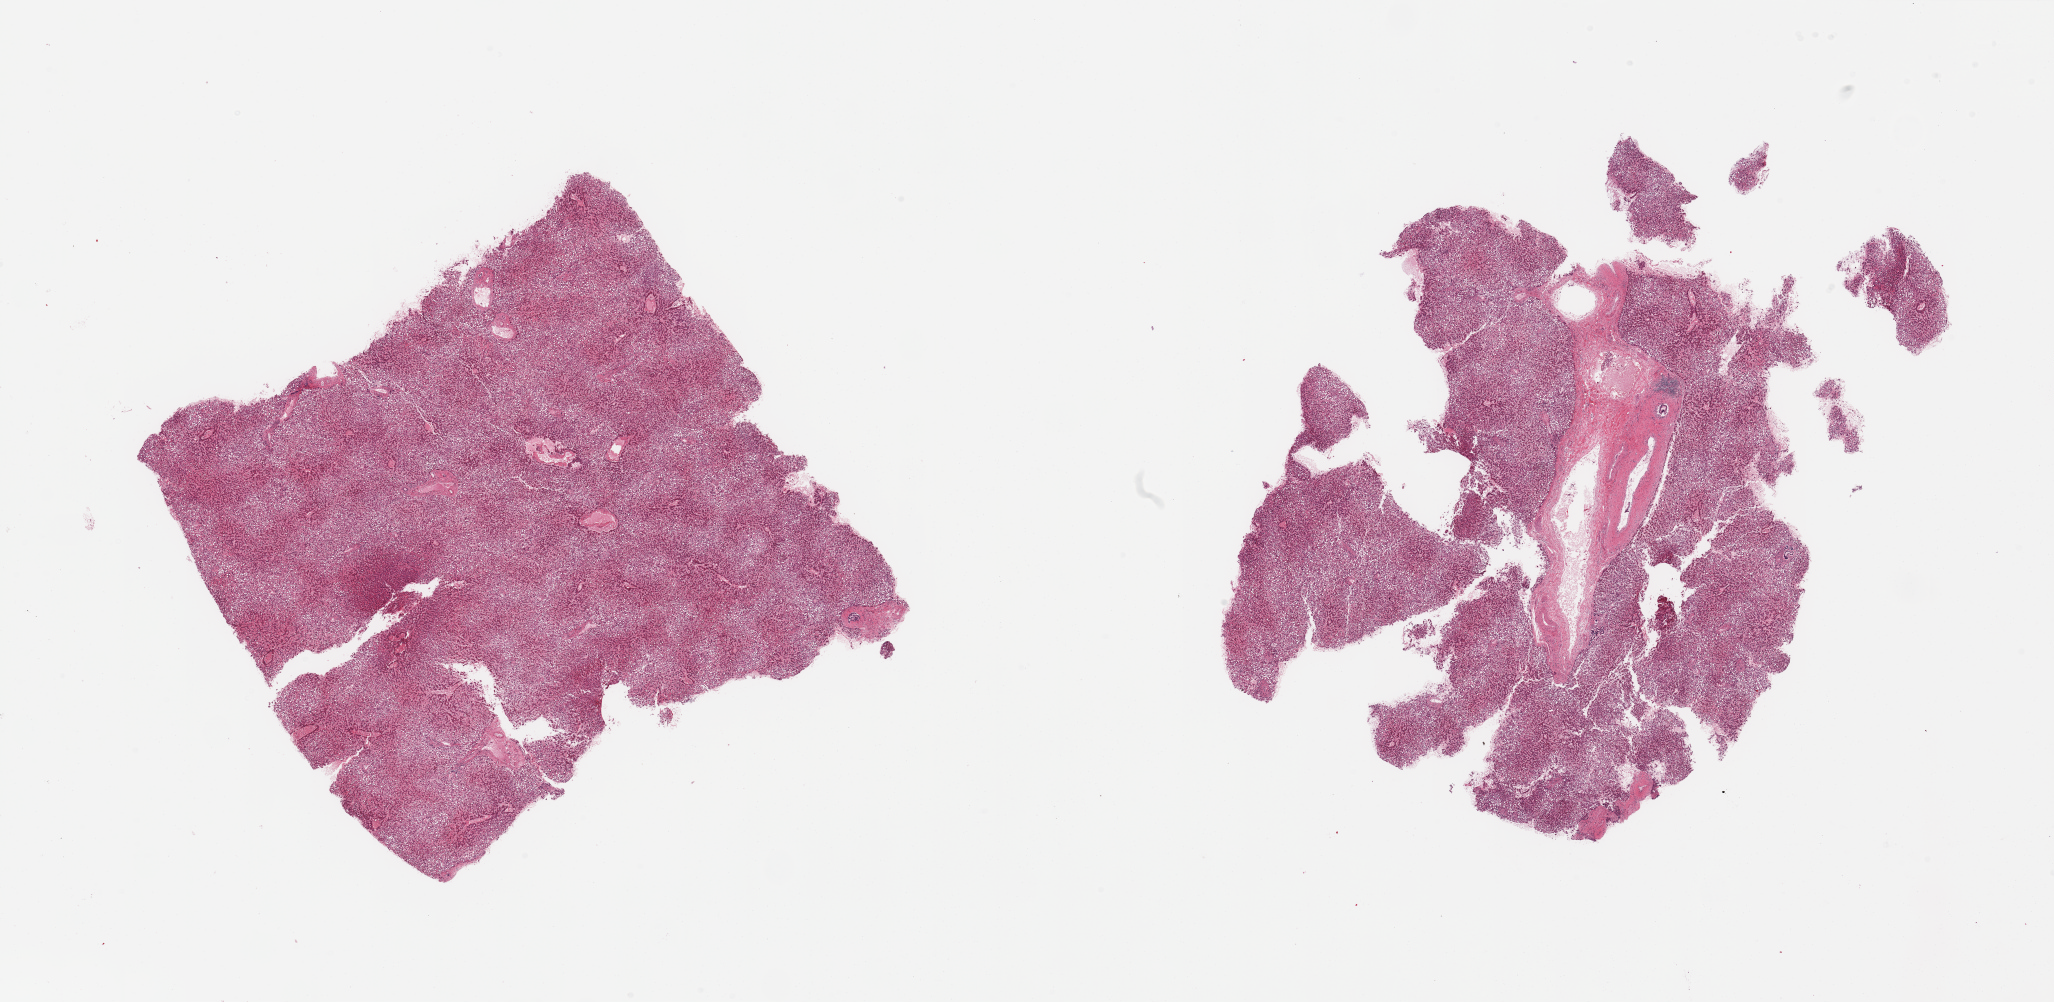
Digitized H&E-stained section, brightfield — shown as a low-resolution overview of the whole scanned area (about 32.5 x 15.8 mm); PAXgene-fixed, paraffin-embedded tissue; target tissue: liver; tissue donor sample. Donor: female.
Reviewer comment on this tissue sample: 2 pieces, diffuse macrovesicular steatosis.